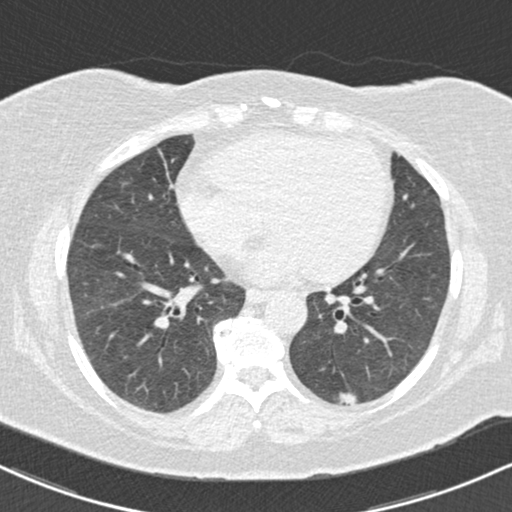
Low-dose screening chest CT, one axial slice. Slice 66 of 147 in the series (ordered by position). Reconstruction kernel B30f. 120 kVp. Lung window (W 1500 / L -600 HU). 2 mm slice thickness. 512 × 512 image matrix, field of view 322 × 322 mm.
Outlined on this slice (expert manual segmentation):
- lesion 1 (tumor, lower lobe of left lung): bounding box <338,392,357,405> (left, top, right, bottom; pixels)